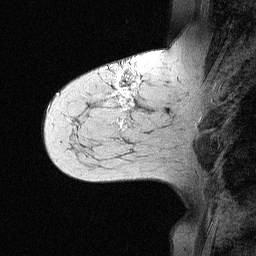
Breast MRI (dynamic contrast-enhanced), one sagittal slice. Dynamic contrast-enhanced study with each time point stored as its own series, time point 2 of 3 at this slice position (early post-contrast, ordered by acquisition time). 1.5 T. TE 4.5 ms, TR 11 ms. 2.06 mm slice thickness. 256 × 256 image matrix, field of view 200 × 200 mm. Female patient, age 55 years. From the clinical record (not read from this slice): setting: breast cancer imaged before/during neoadjuvant chemotherapy; receptor status: triple-negative.
Structures marked on this image (semi-automatic segmentation, software-assisted and operator-edited):
- analysis volume of interest (the breast-tissue region the enhancement analysis was run in; not a lesion): bounding box <71,63,147,145> (left, top, right, bottom; pixels)
- tumour enhancement mask (voxels above the 90 % enhancement threshold inside the analysis volume of interest): <108,68,141,127>